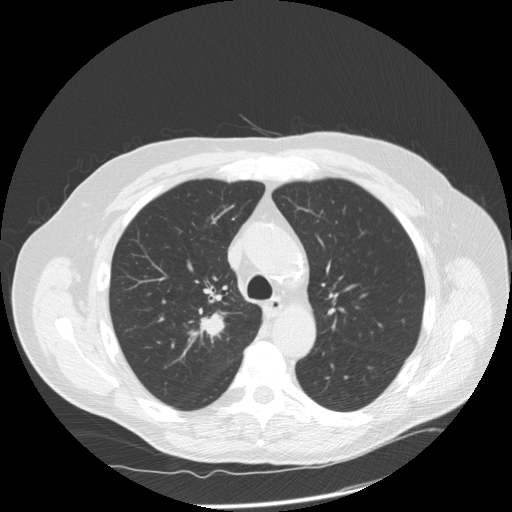
Low-dose screening chest CT, one axial slice; 120 kVp; lung window (W 1500 / L -600 HU); 2.5 mm slice thickness; 512 × 512 image matrix.
Structures marked on this image (manually delineated by an expert):
- lesion 1 (tumor, upper lobe of right lung): bounding box (x1, y1, x2, y2) in pixels: (201, 314, 224, 336)